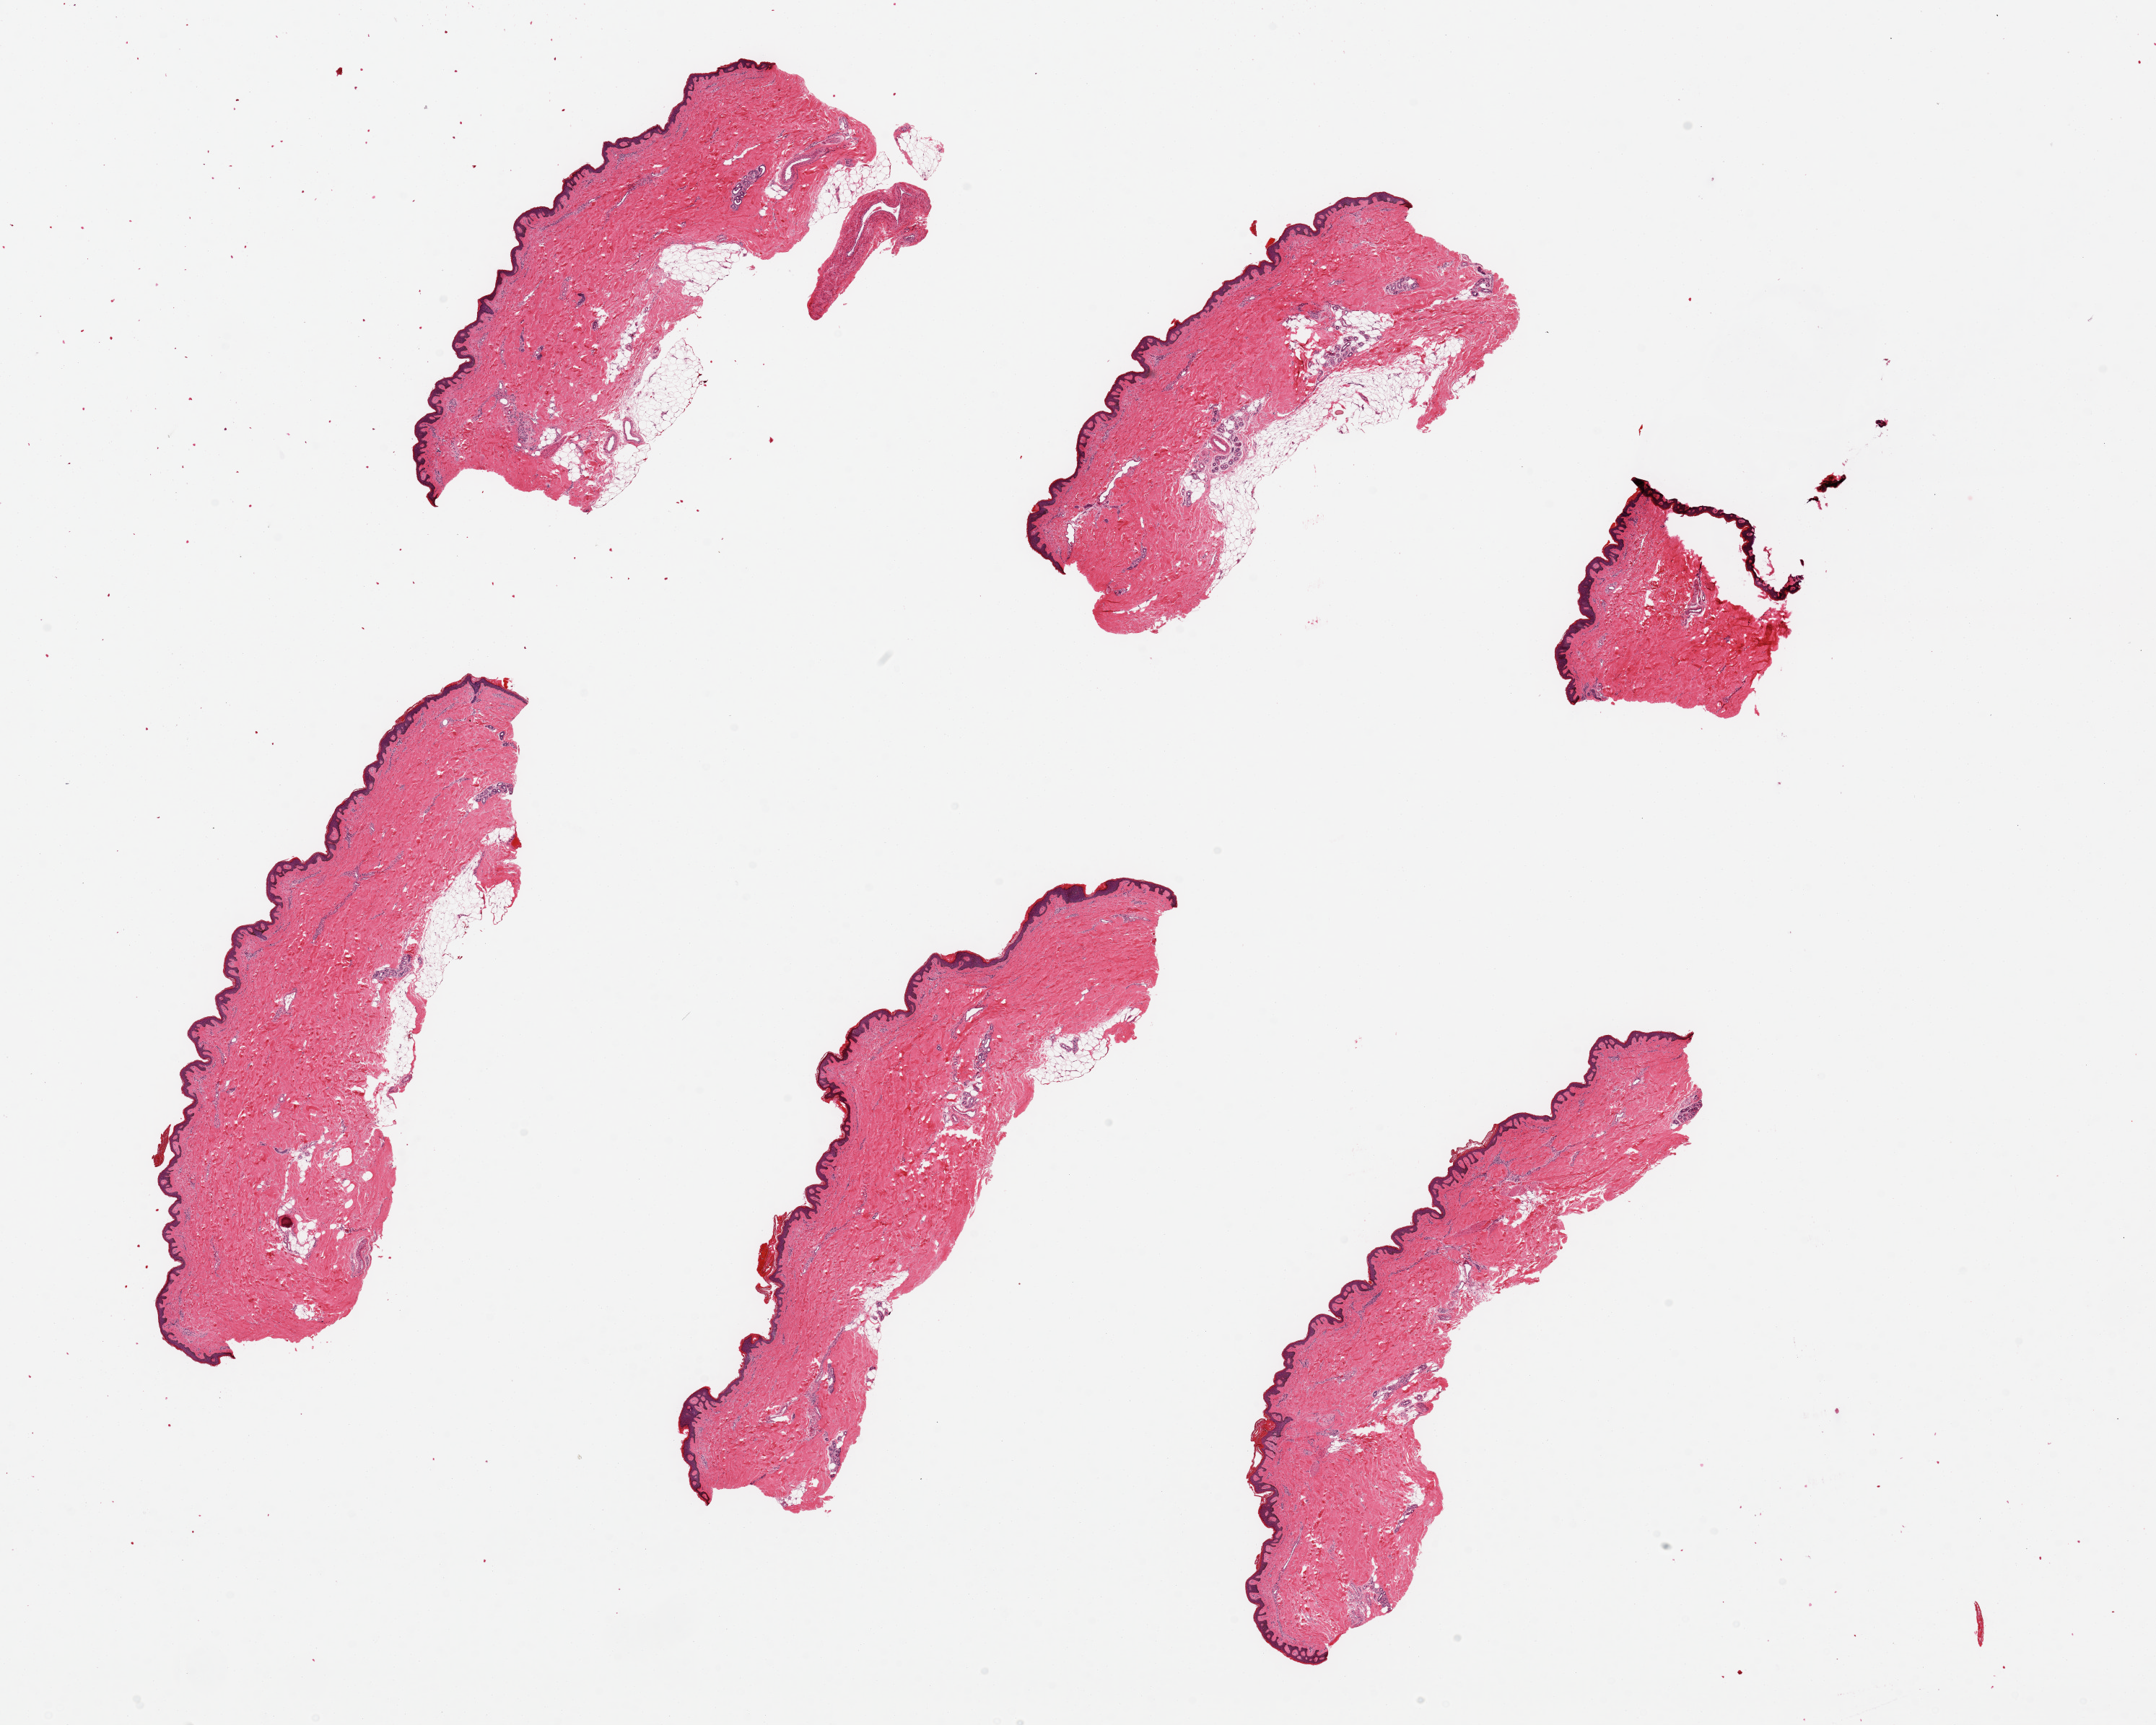
Whole-slide image, hematoxylin and eosin (H&E) stain, brightfield, shown as a low-resolution overview of the whole scanned area (about 23.6 x 18.9 mm, from a 20x scan), PAXgene-fixed paraffin-embedded (PFPE) section, sampled site (target tissue): skin of lower leg, donor tissue sample. Donor: male.
- review note (as recorded): 5 pieces + one fragment, ~8x2mm. Squamous epithelium is ~2-3% of thickness